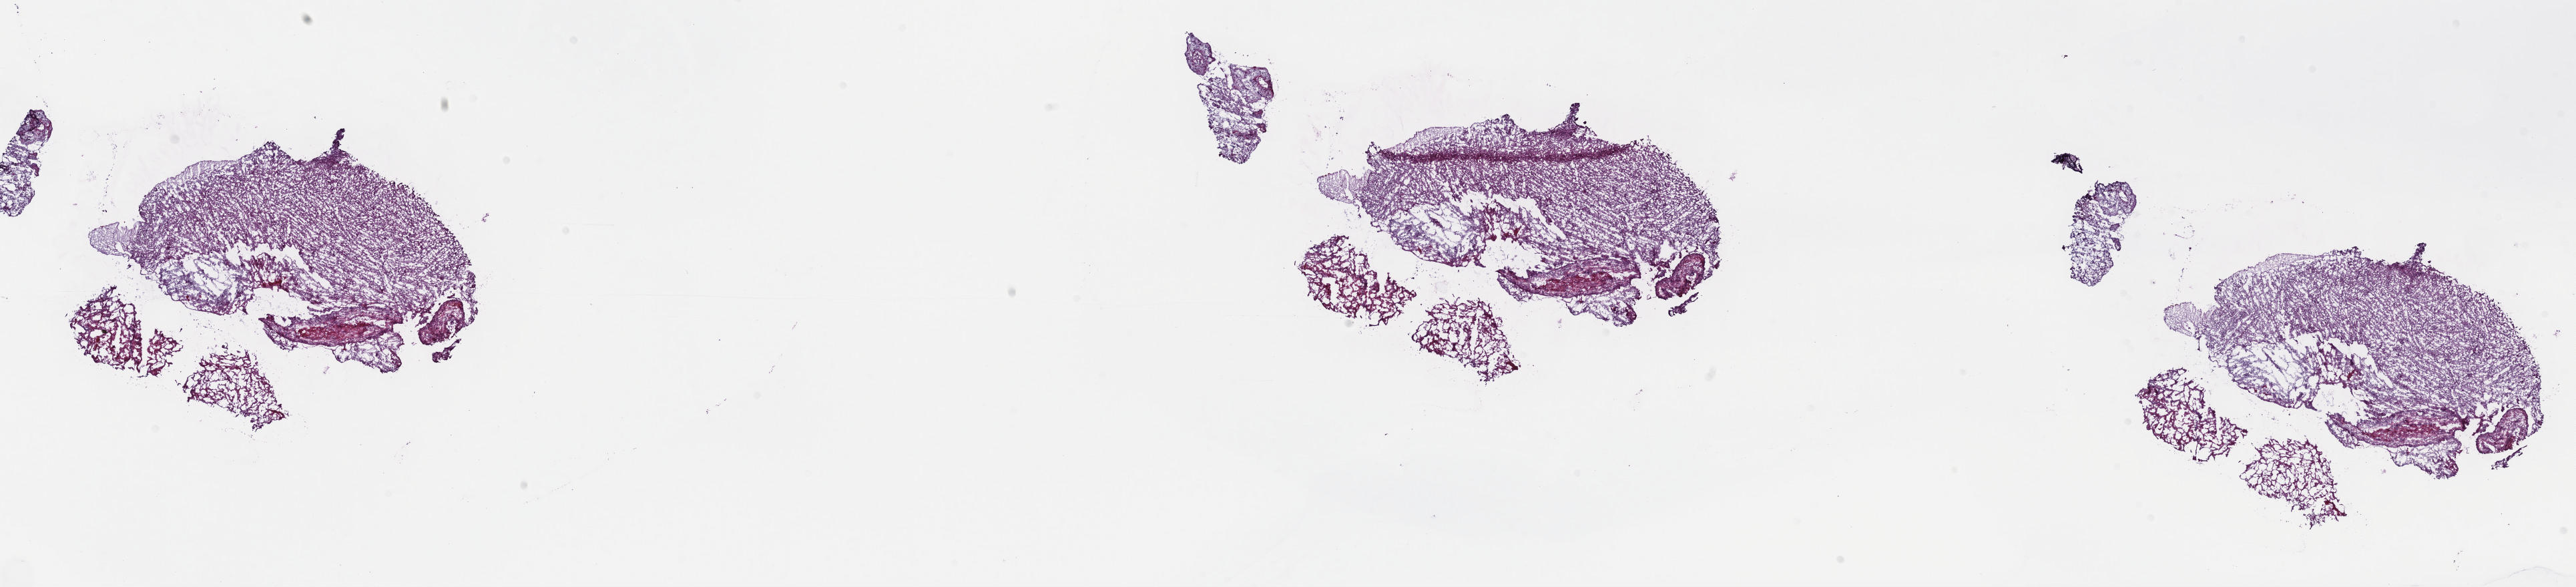
Whole-slide histology image, H&E — low-resolution overview of the scanned area, about 31.2 x 7.1 mm (from a 40x scan), frozen section, brain, primary tumour sample. Female, age 54 years at initial diagnosis. Slide review estimates, as recorded: tumour cells 50%, tumour nuclei 90%, normal cells 10%, stromal cells 40%, necrosis 0%. Infiltration values recorded for this section: lymphocyte infiltration 2%, monocyte infiltration 2%, neutrophil infiltration 0%.
- histologic diagnosis: Glioblastoma